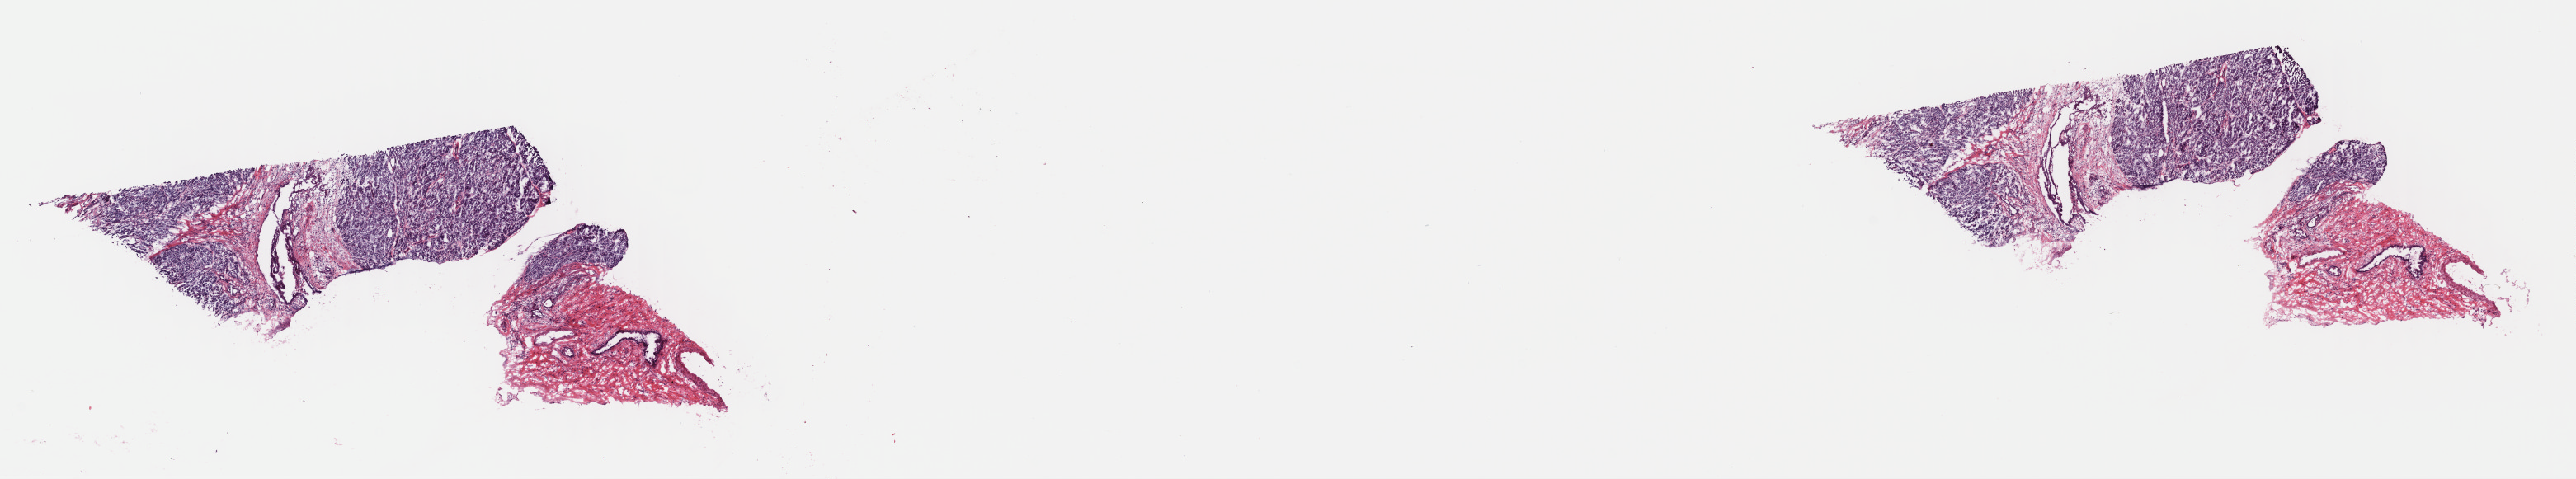
H&E whole-slide image, shown as a low-resolution overview of the whole scanned area (about 24.6 x 4.6 mm, slide scanned at 40x), frozen section, pancreas, primary tumour sample. Male patient; age at initial diagnosis 64 years. Histologic grade: G2 (moderately differentiated). Composition of this section per pathologist review: tumour cells 8%, tumour nuclei 12%, normal cells 45%, stromal cells 45%, necrosis 2%. Inflammatory infiltration, as recorded: lymphocyte infiltration 8%, monocyte infiltration 1%, neutrophil infiltration 1%.
- histologic diagnosis: Infiltrating duct carcinoma, NOS (head of pancreas)
- TNM: T3 N1 MX
- AJCC pathologic stage: IIB (7th edition)